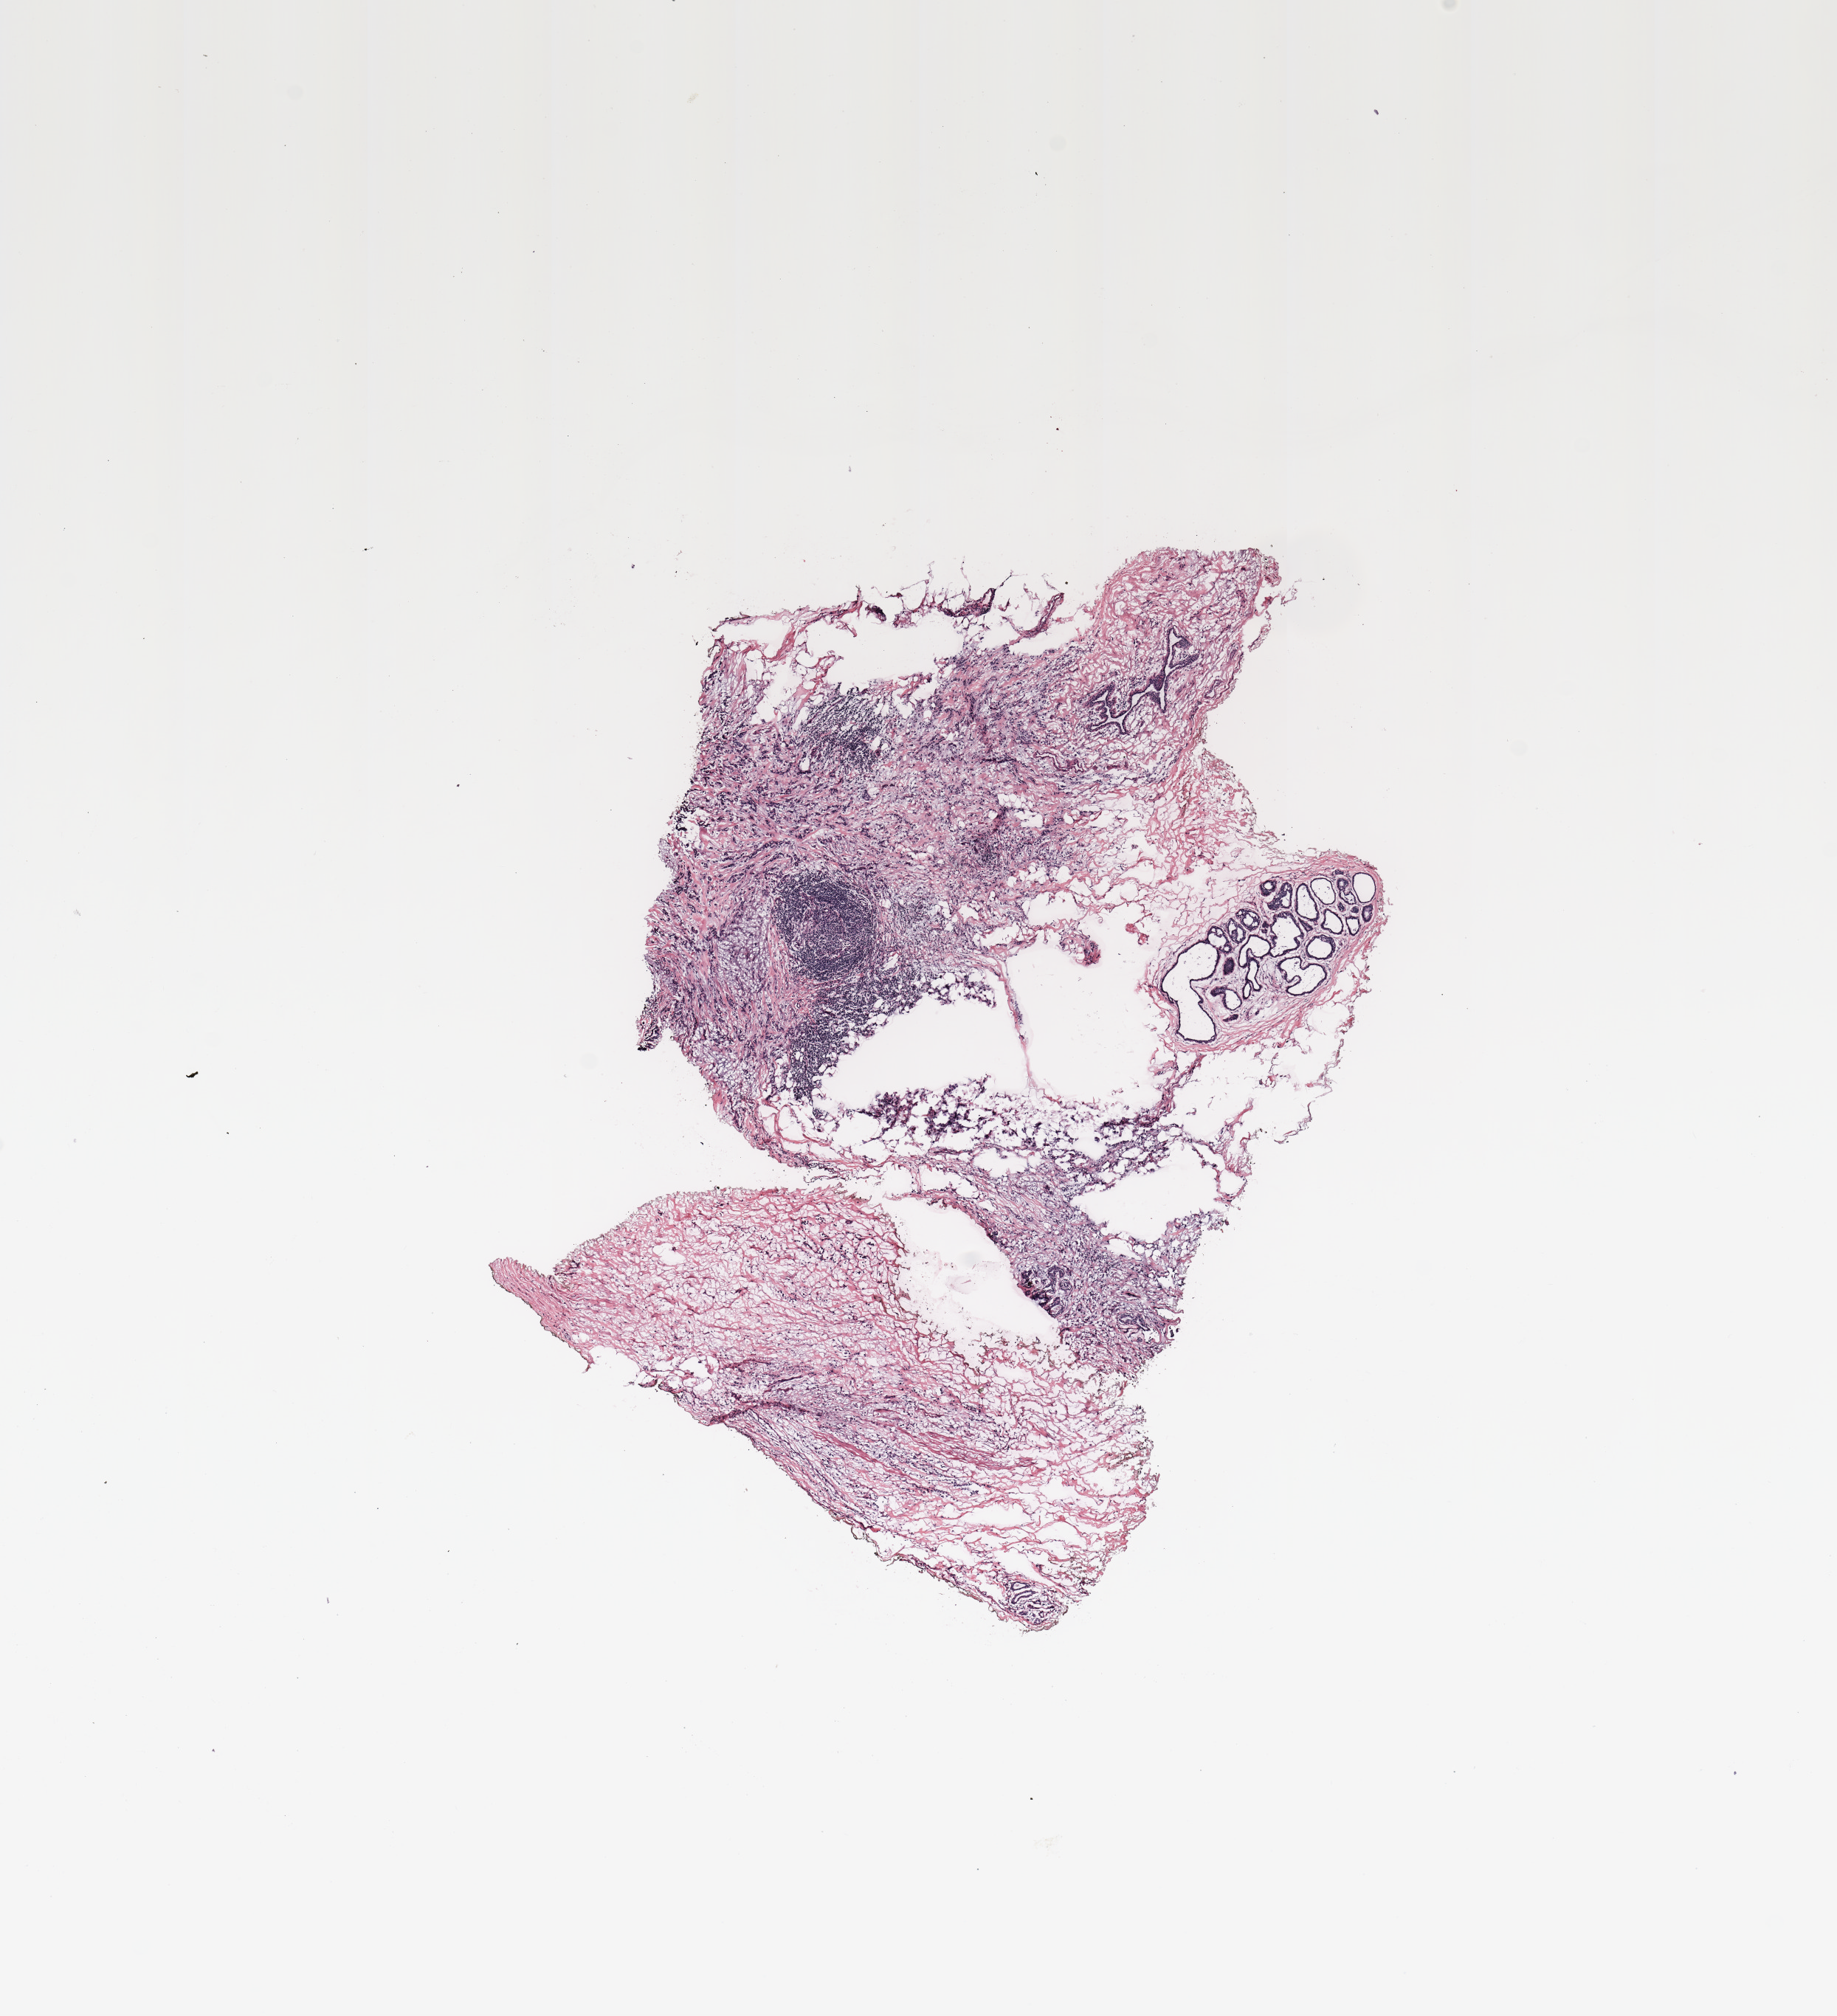
Digitized H&E tissue section (whole slide), shown as a low-resolution overview of the whole scanned area (about 9.8 x 10.8 mm). Breast, tissue type not recorded.
• patient diagnosis (cohort enrolment): breast cancer (breast)